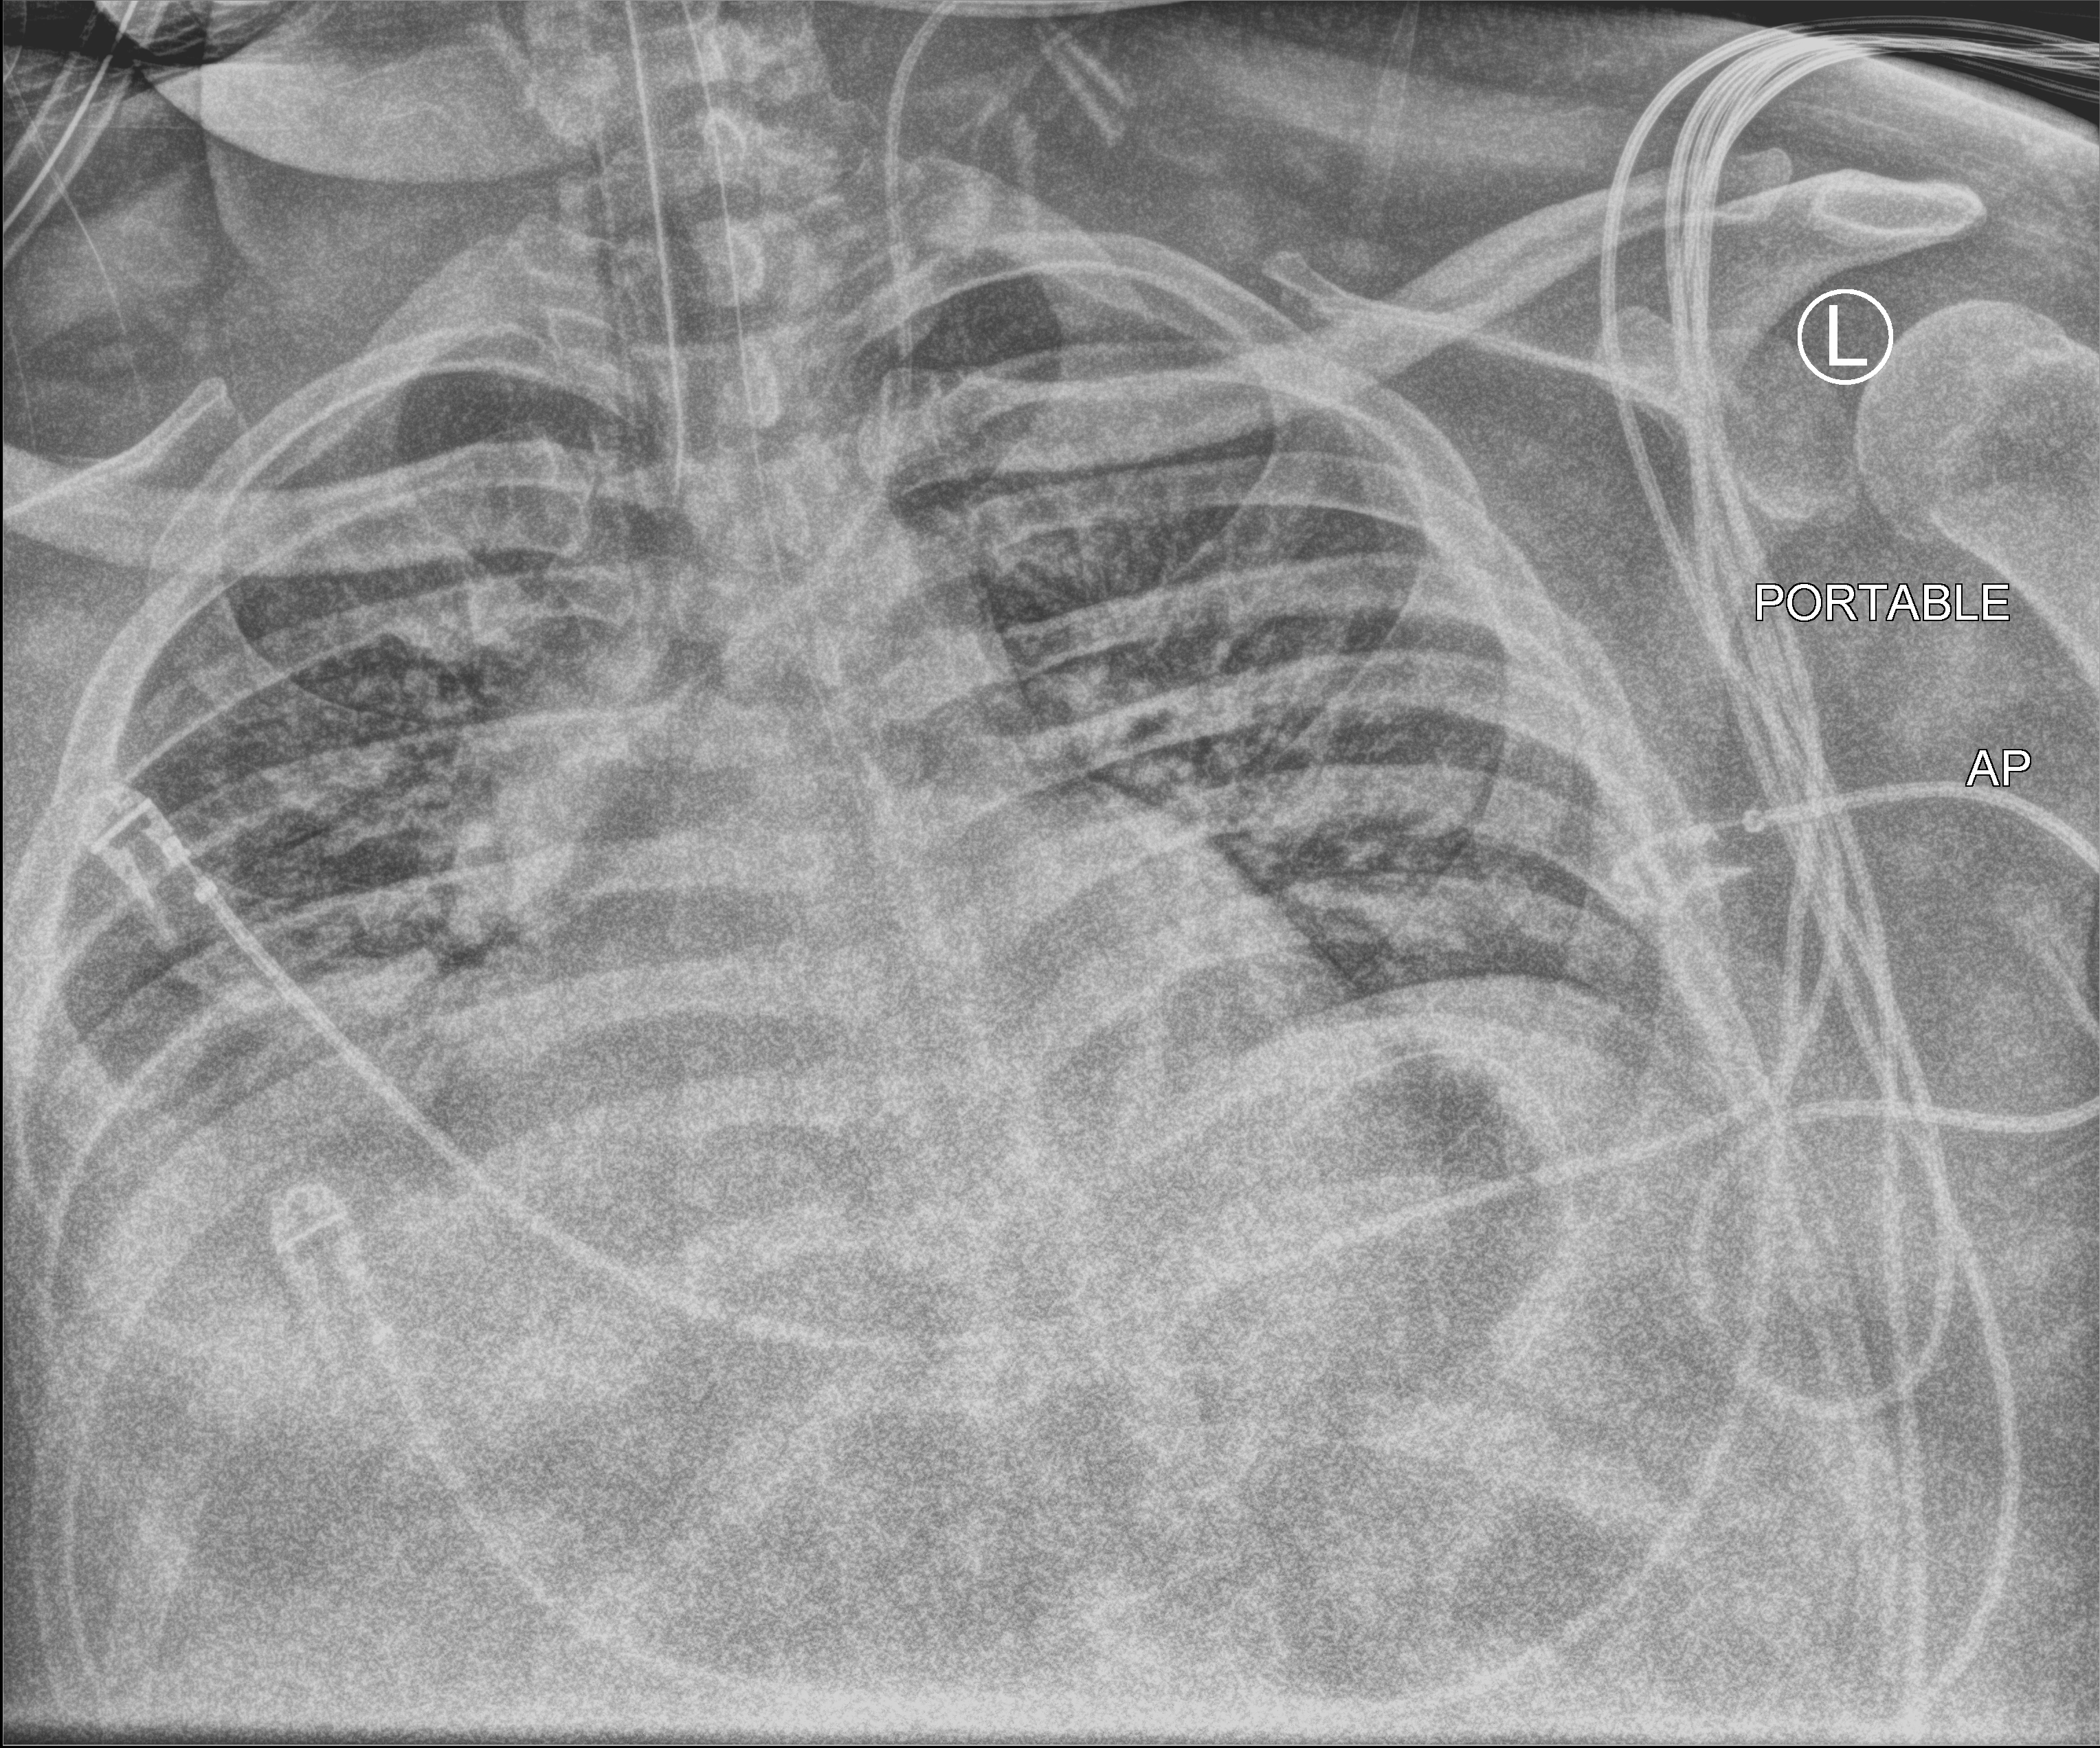
Bedside chest radiograph (computed radiography); anteroposterior (AP) projection. Male patient hospitalised with COVID-19, age 18–59 years.
Hospital-stay facts (about this admission, not read from this image; timing relative to this image not recorded): diabetes (admission record): yes; COPD (admission record): yes; length of hospital stay: 69 days.